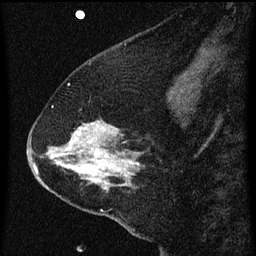
Breast MRI (dynamic contrast-enhanced), one sagittal slice; position 20 of 60 along the scan axis; dynamic contrast-enhanced series, image 2 of 3 at this slice position (ordered by acquisition); 1.5 T; TE 4.2 ms, TR 8 ms; 256 × 256 image matrix, field of view 180 × 180 mm. Patient: female, 47 years.
Structures marked on this image (semi-automatically segmented with operator editing):
- analysis volume of interest (the breast-tissue region the enhancement analysis was run in; not a lesion): bounding box <36,106,146,213> (left, top, right, bottom; pixels)
- tumour enhancement mask (voxels above the 70 % enhancement threshold inside the analysis volume of interest): <36,124,139,191>